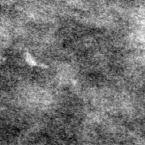
Region of interest cut from a scanned film mammogram (one marked finding); left breast; CC view; BI-RADS breast density category 2 (scale 1–4).
- Finding: calcifications, morphology fine linear branching, distribution clustered / linear; BI-RADS assessment category 4; subtlety rating 3 on a 1 (subtle) to 5 (obvious) scale; pathology (as recorded): malignant.